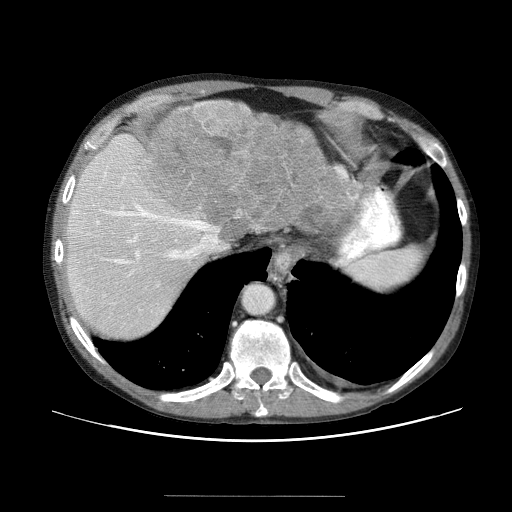
Contrast-enhanced abdominal CT (liver protocol), one axial slice; position 50 of 69 along the scan axis; reconstruction kernel STANDARD; 120 kVp; soft-tissue window (W 400 / L 40 HU); 2.5 mm slice thickness; 512 × 512 image matrix, field of view 380 × 380 mm. From the clinical record (not read from this slice): diagnosis: hepatocellular carcinoma (patient treated with transarterial chemoembolisation; whether this scan precedes or follows treatment is not stated here); TNM stage (as recorded): Stage-IVB; Child-Pugh class: B; tumour nodularity: multinodular.
Annotated regions visible in this slice (semi-automatically segmented with operator editing):
- liver parenchyma outside the tumour (the mass and vessels are separate outlines, so this box may not span the whole liver): bounding box [x1, y1, x2, y2] px = [64, 132, 360, 346]
- mass: [145, 98, 364, 247]
- liver vessels: [94, 181, 155, 312]